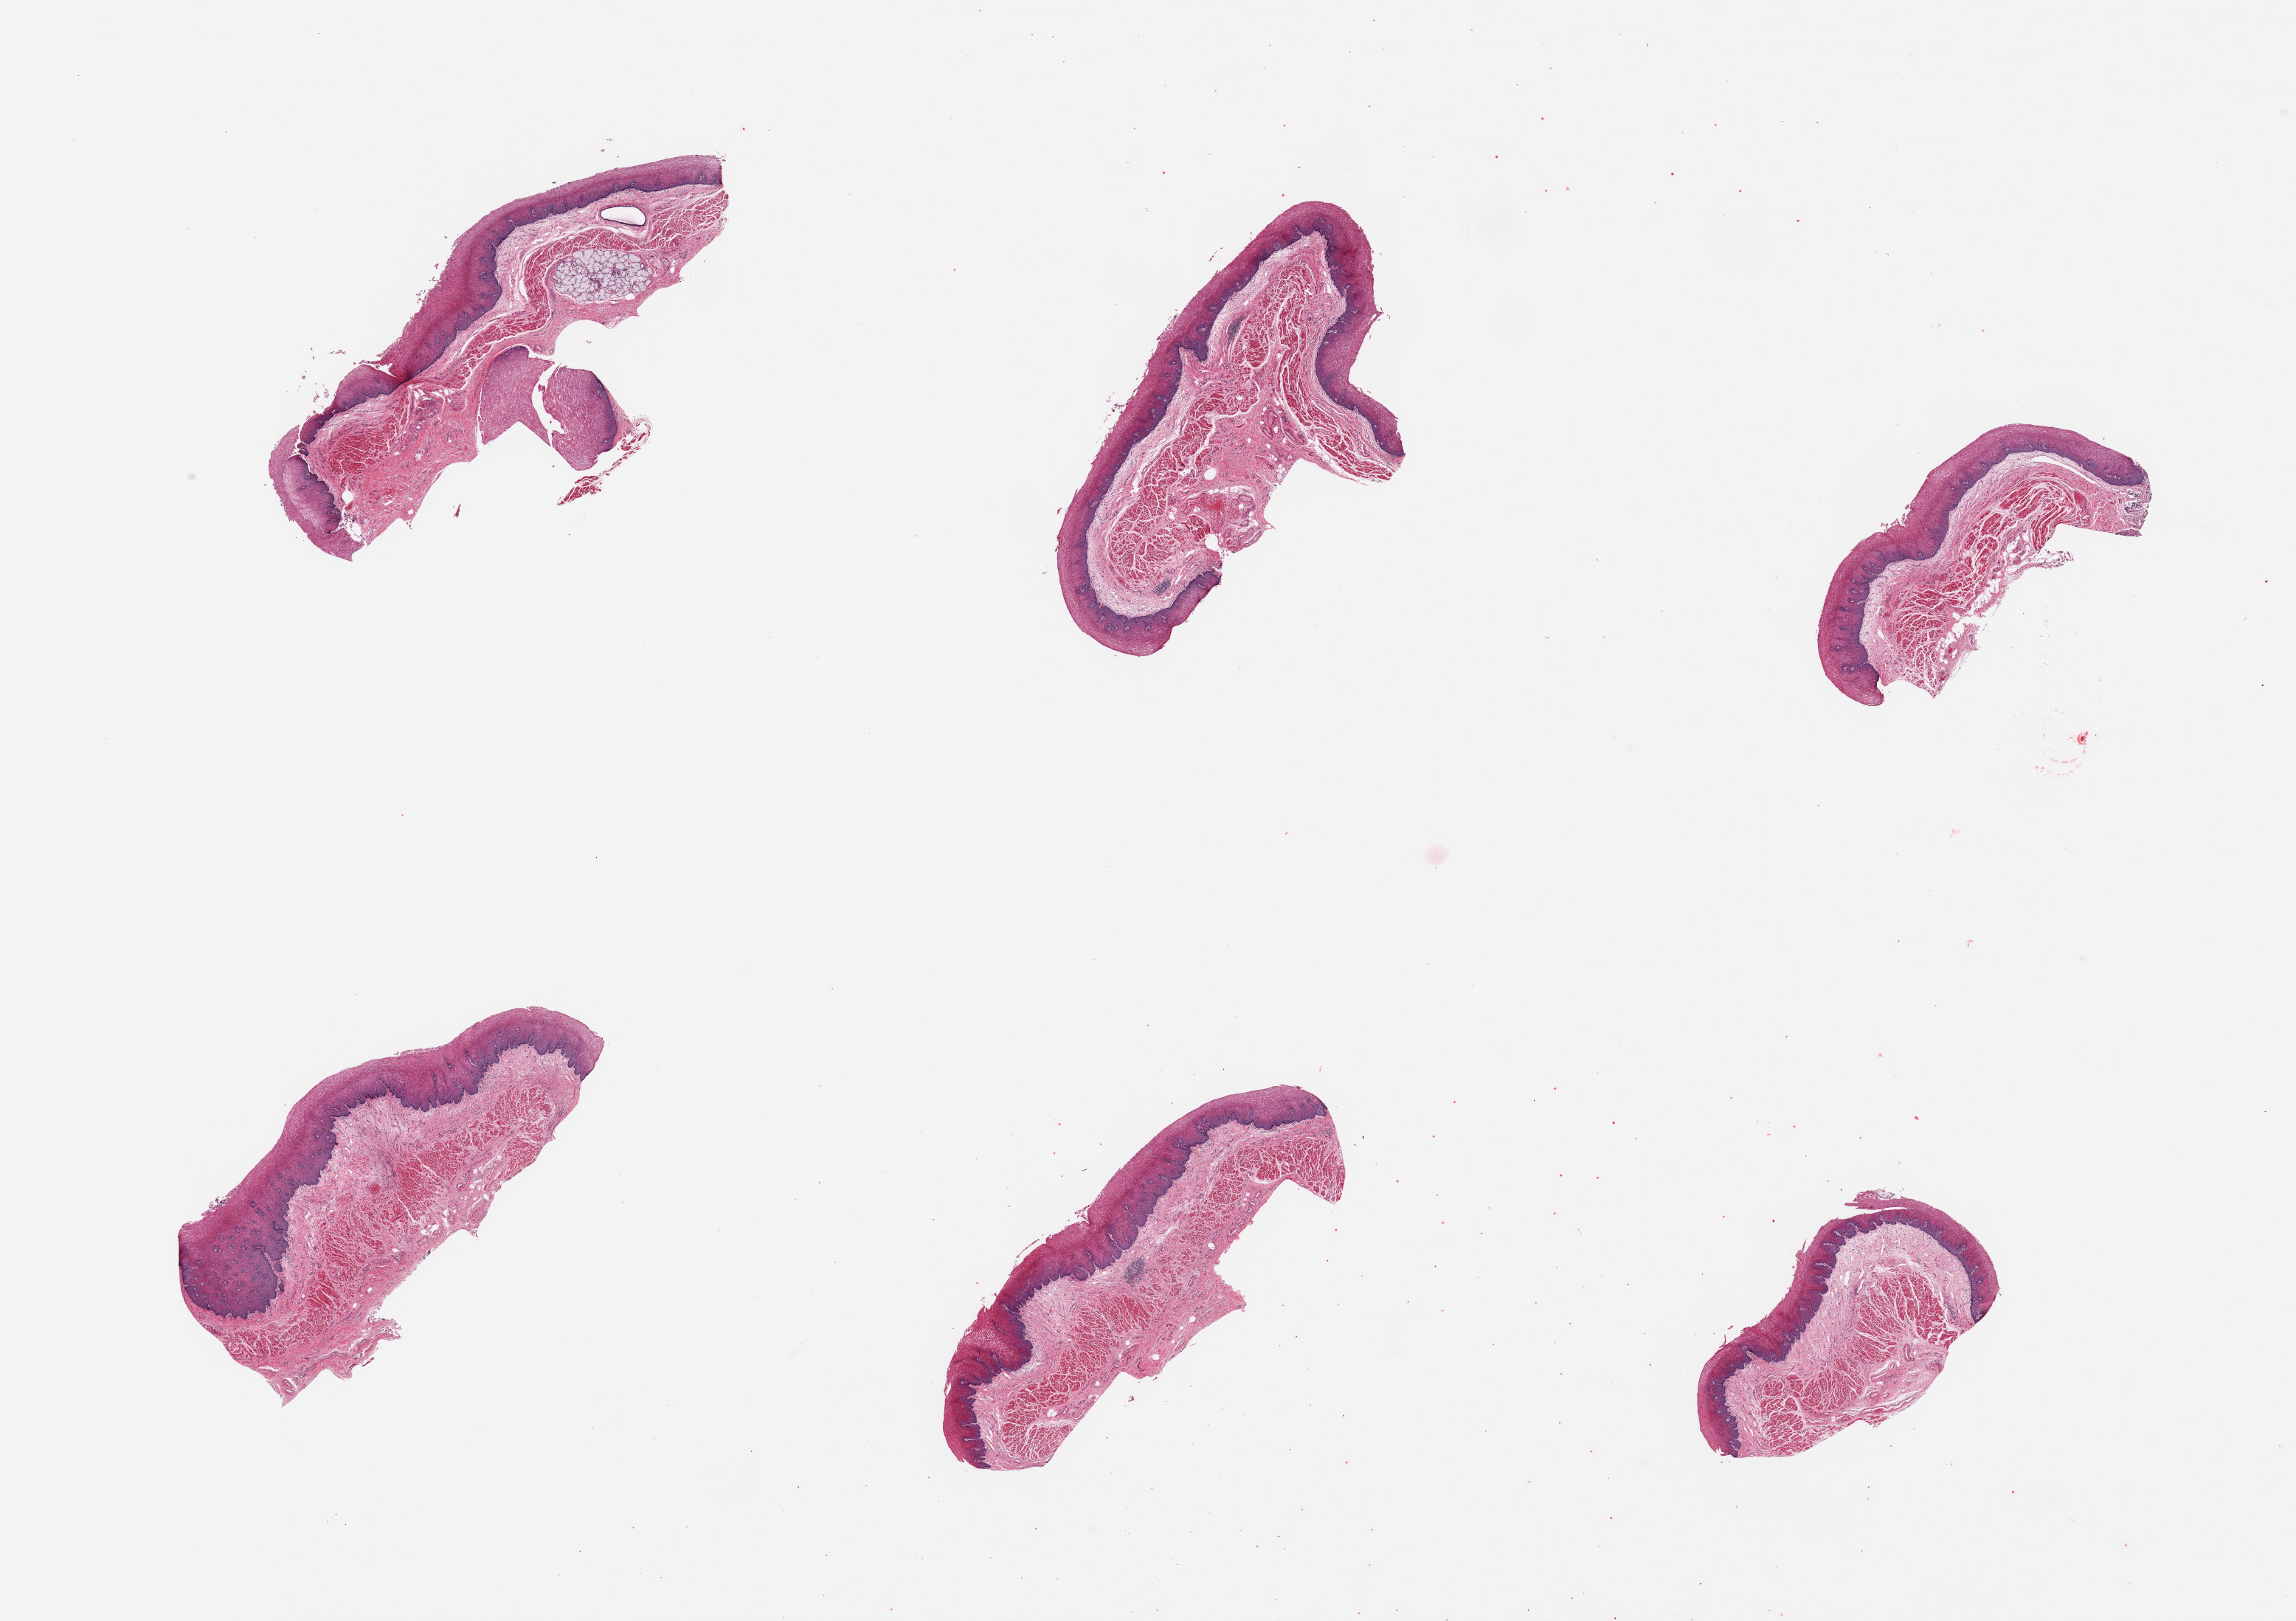
Whole-slide image, haematoxylin and eosin stain, brightfield, whole scanned area (about 24.6 x 17.4 mm) shown as a low-resolution overview; PAXgene-fixed paraffin-embedded (PFPE) section; target tissue: esophageal mucous membrane; tissue donor sample. Donor sex: male.
Pathologist's review note for this sample: 6 pieces; 1 large (1 mm) submucosal gland.